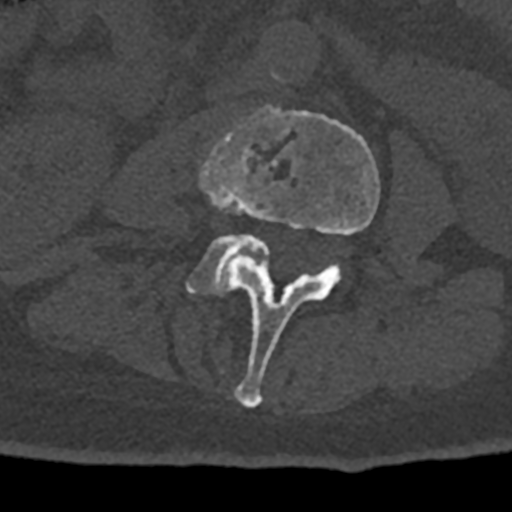
CT including the spine, one axial slice. Position 304 of 797 along the scan axis. Reconstruction kernel Br40s/3. Bone window (W 1800 / L 400 HU). 0.5 mm slice thickness. 512 × 512 image matrix, field of view 160 × 160 mm. Patient: male, 74 years. Case-level facts recorded for this patient, not image findings: primary cancer: renal.
Annotated regions visible in this slice (semi-automatic segmentation, software-assisted and operator-edited):
- L3 vertebra: bounding box [x1, y1, x2, y2] px = [200, 106, 380, 408]
- L4 vertebra: [186, 234, 269, 296]